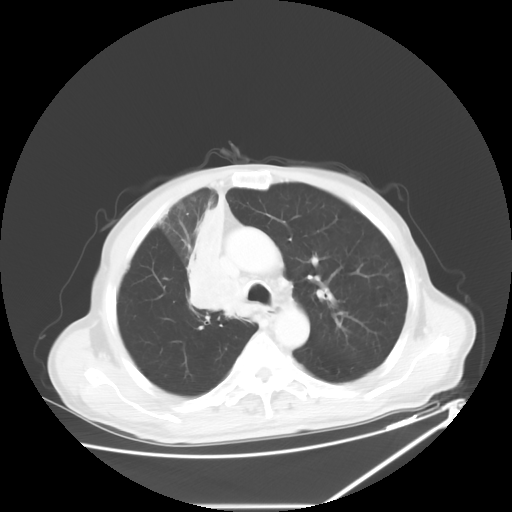
Chest CT, one axial slice. Position 43 of 60 along the scan axis. Reconstruction kernel STANDARD. 120 kVp. Lung window (W 1500 / L -600 HU). 5 mm slice thickness. 512 × 512 image matrix, field of view 410 × 410 mm. Male patient, age 73 years. From the clinical record (not read from this slice): clinical TNM (as recorded): T2a N1 M0.
Structures marked on this image (bounding box drawn by a radiologist):
- lung tumour (recorded histology: squamous cell carcinoma): box from (x=185, y=185) to (x=248, y=322) px